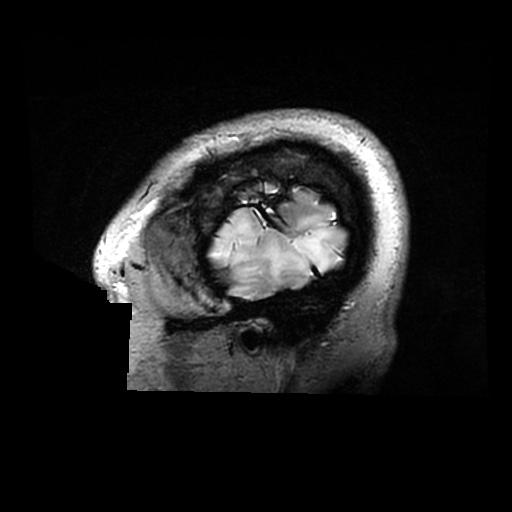
Brain MRI from a brain-tumour surgery series, one sagittal slice. Slice 255 of 320 in the series (ordered by position). 0.6 mm slice thickness. 512 × 512 image matrix, field of view 240 × 240 mm. From the clinical record (not read from this slice): histopathology: Astrocytoma; WHO grade: 2; IDH mutation: yes.
Annotated regions visible in this slice (outlined manually by an expert reader):
- tumour: bounding box [x1, y1, x2, y2] px = [211, 212, 344, 283]